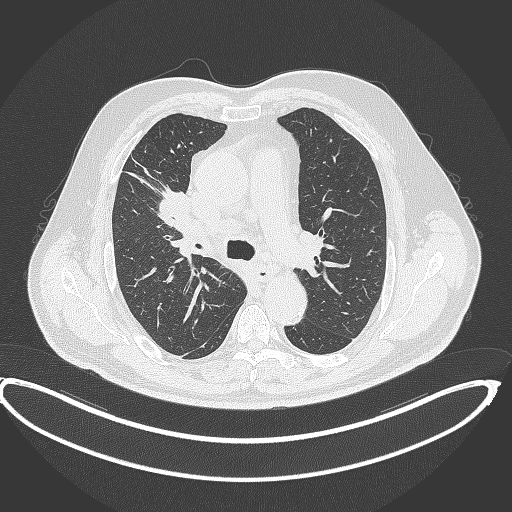
Chest CT, one axial slice. Position 270 of 390 along the scan axis. Reconstruction kernel B70f. 120 kVp. Lung window (W 1500 / L -600 HU). 1 mm slice thickness. 512 × 512 image matrix. Patient: male, 62 years. Case-level facts recorded for this patient, not image findings: clinical TNM (as recorded): T1c N3 M1c.
Outlined on this slice (rectangle marked by the reading radiologist):
- lung tumour (recorded histology: adenocarcinoma): bounding box [x1, y1, x2, y2] px = [157, 185, 194, 236]